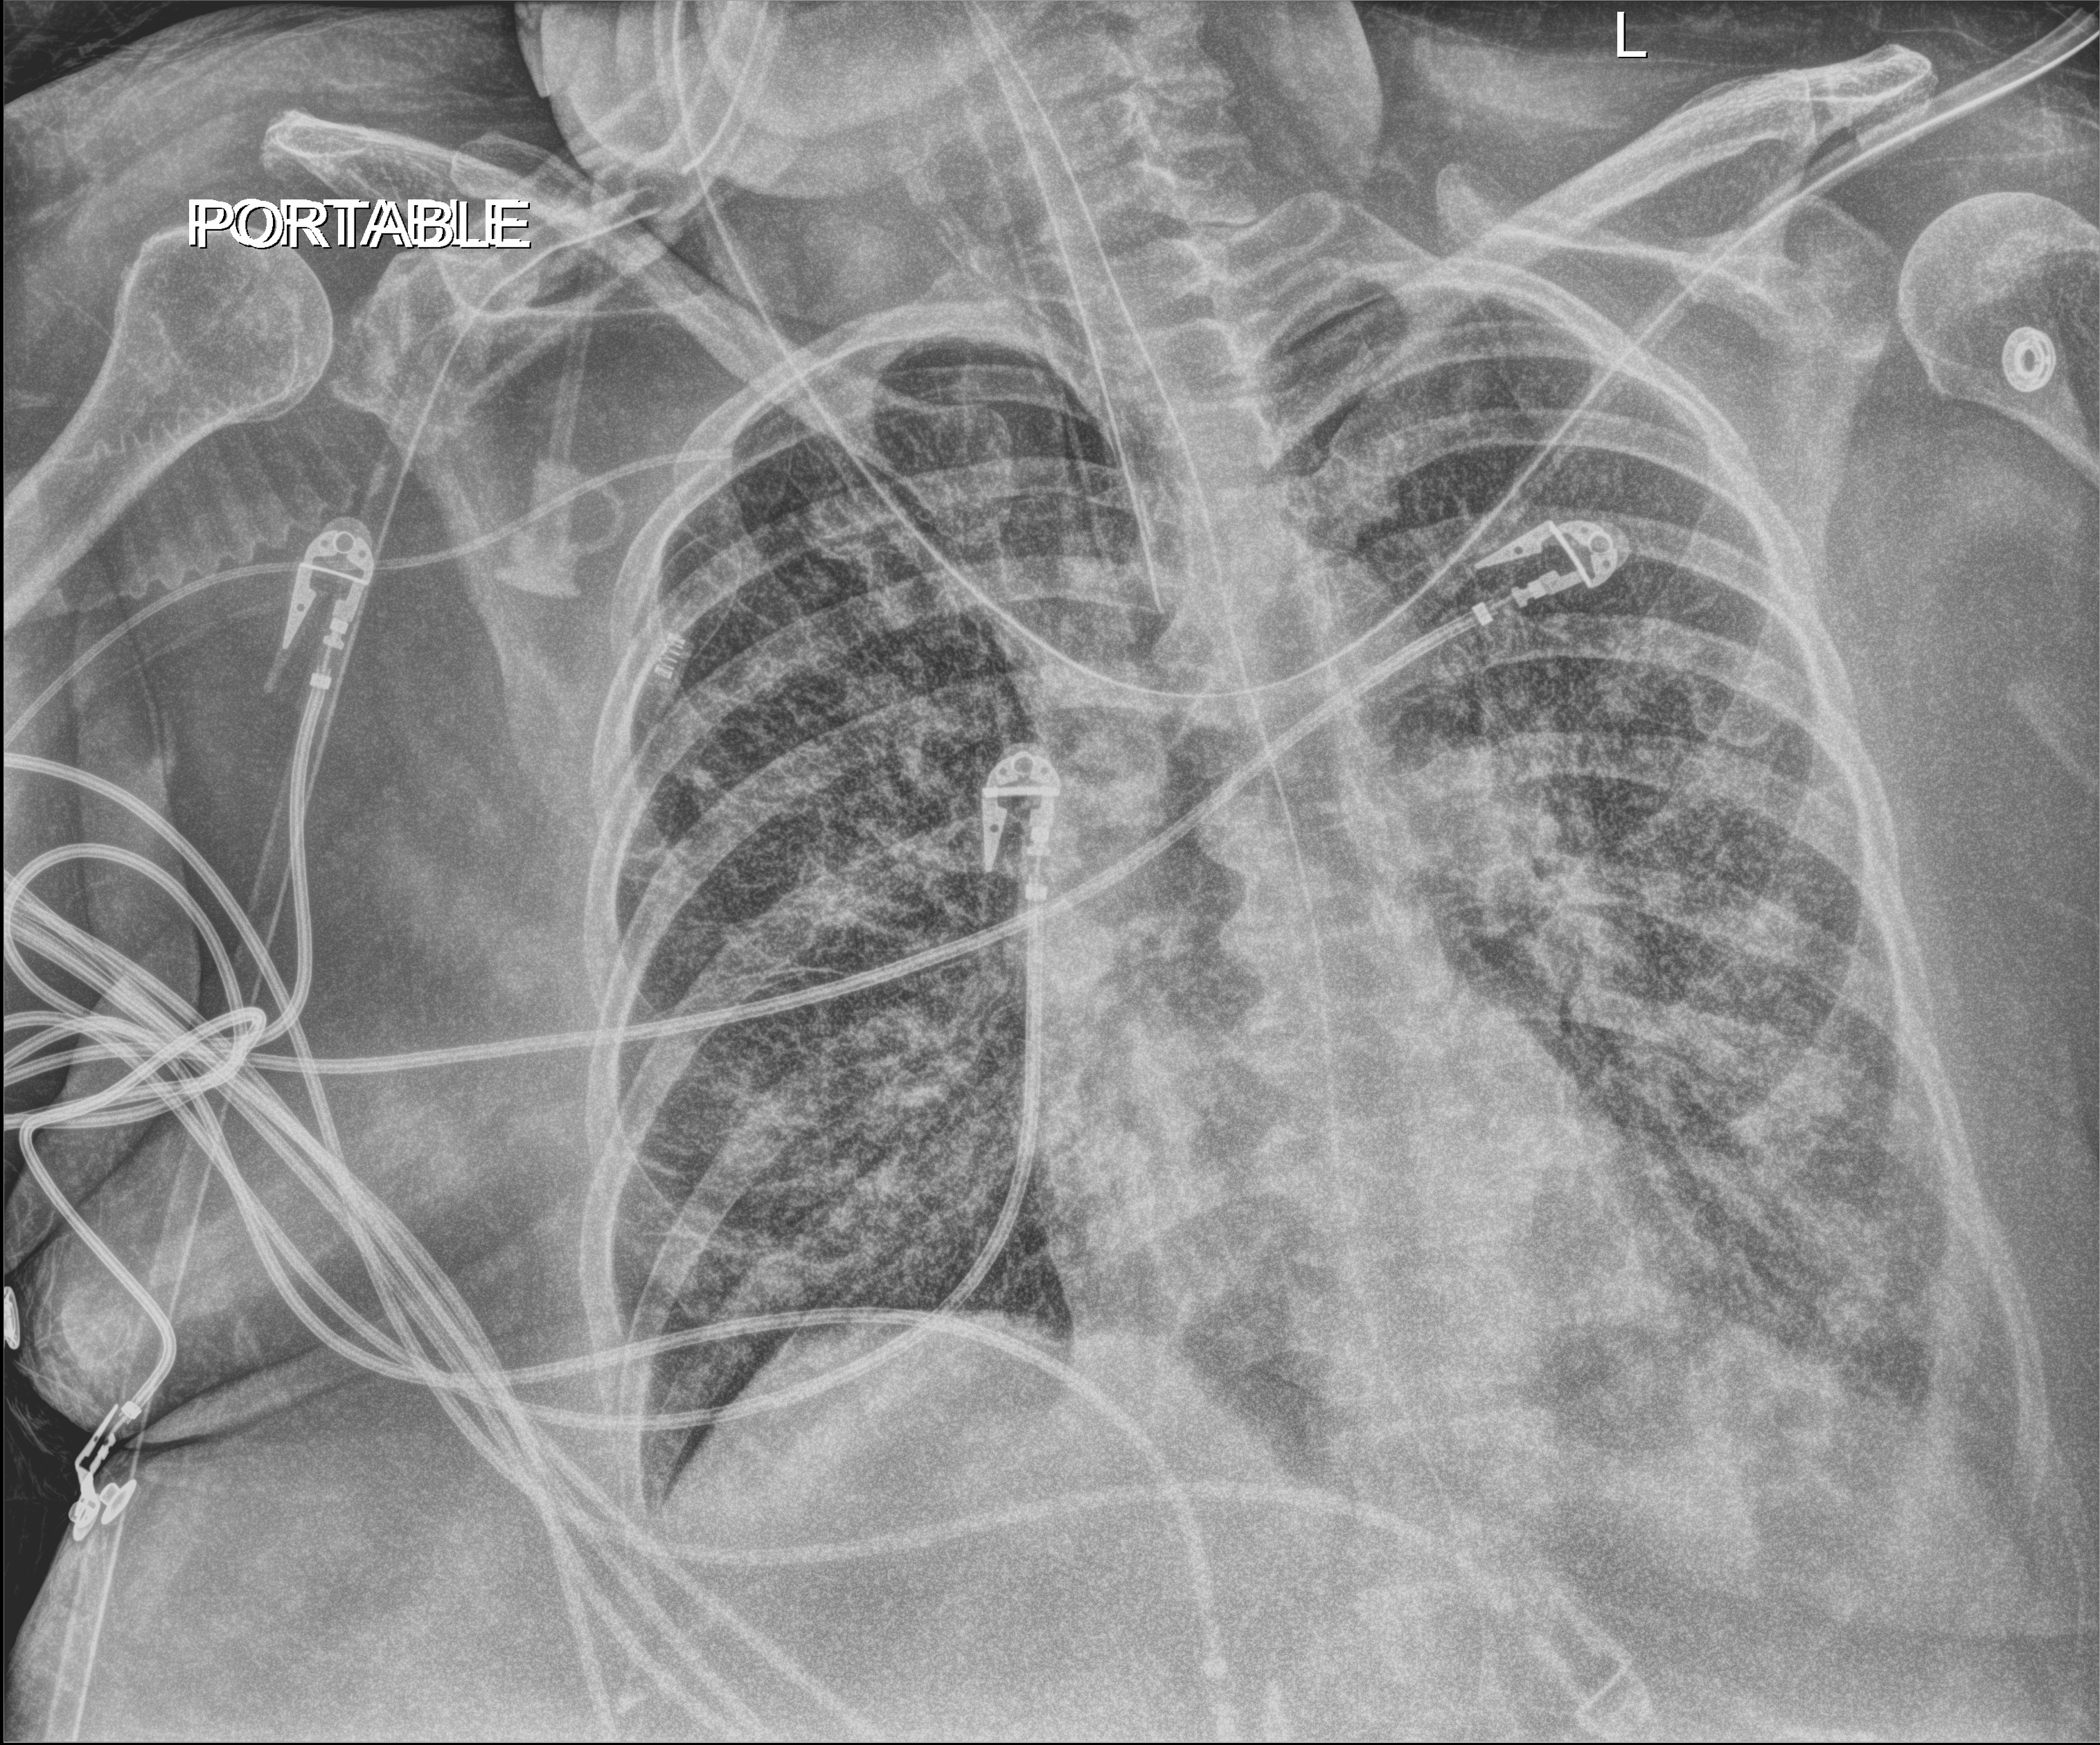
Chest X-ray (portable), anteroposterior (AP) projection. Female patient hospitalised with COVID-19, age 60–74 years.
From the hospital-stay record, not from the radiograph (when in the stay this image was taken is not recorded): mechanically ventilated during this hospital stay: yes.